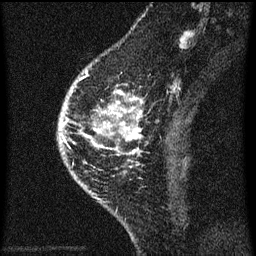
Breast MRI (dynamic contrast-enhanced), one sagittal slice. Position 20 of 60 along the scan axis. Dynamic contrast-enhanced series, image 2 of 3 at this slice position (ordered by acquisition). 1.5 T. TE 4.2 ms, TR 8 ms. 2 mm slice thickness. 256 × 256 image matrix, field of view 180 × 180 mm. Patient: female, 46 years.
Structures marked on this image (semi-automatically segmented with operator editing):
- analysis volume of interest (the breast-tissue region the enhancement analysis was run in; not a lesion): bounding box (x1, y1, x2, y2) in pixels: (83, 68, 145, 195)
- tumour enhancement mask (voxels above the 70 % enhancement threshold inside the analysis volume of interest): (84, 70, 143, 175)